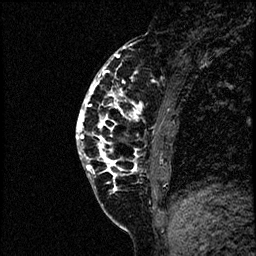
Breast MRI (dynamic contrast-enhanced), one sagittal slice; position 20 of 60 along the scan axis; dynamic contrast-enhanced study with each time point stored as its own series, time point 2 of 4 at this slice position (early post-contrast, ordered by acquisition time); 1.5 T; TE 4.2 ms, TR 17.6 ms; 2 mm slice thickness; 256 × 256 image matrix. Patient: female, 40 years. Case-level facts recorded for this patient, not image findings: setting: breast cancer imaged before/during neoadjuvant chemotherapy; receptor status: HER2-positive.
Outlined on this slice (semi-automatic segmentation, software-assisted and operator-edited):
- analysis volume of interest (the breast-tissue region the enhancement analysis was run in; not a lesion): bounding box <77,56,197,205> (left, top, right, bottom; pixels)
- tumour enhancement mask (voxels above the 100 % enhancement threshold inside the analysis volume of interest): <77,56,144,177>